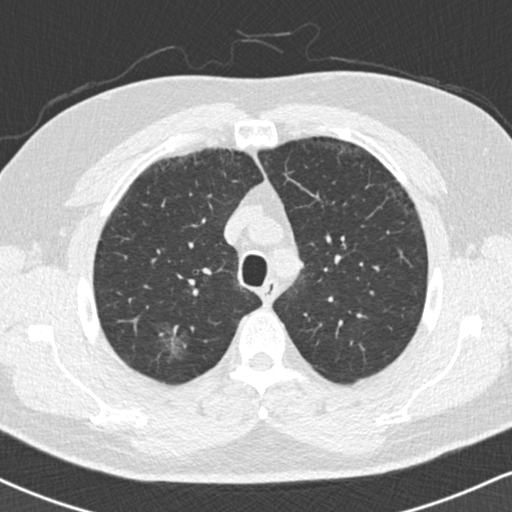
Low-dose screening chest CT, one axial slice; slice 129 of 169 in the series (ordered by position); reconstruction kernel B30f; 120 kVp; lung window (W 1500 / L -600 HU); 512 × 512 image matrix, field of view 320 × 320 mm.
Structures marked on this image (manually delineated by an expert):
- lesion 1 (tumor, upper lobe of right lung): bounding box [x1, y1, x2, y2] px = [160, 323, 185, 356]